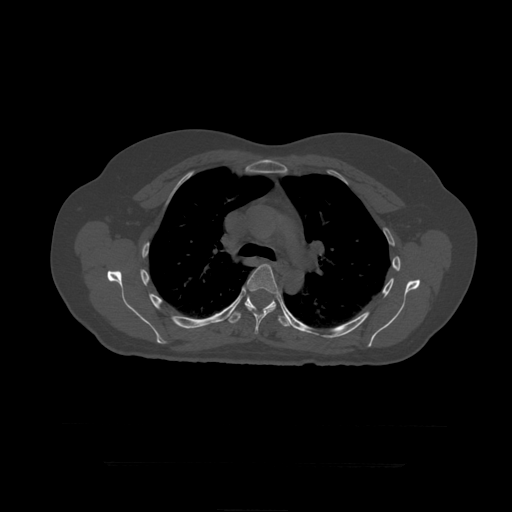
CT including the spine, one axial slice. Slice 313 of 399 in the series (ordered by position). Reconstruction kernel STANDARD. Bone window (W 1800 / L 400 HU). 1.25 mm slice thickness. 512 × 512 image matrix. Patient age 41 years. Case-level facts recorded for this patient, not image findings: primary cancer: breast.
Outlined on this slice (semi-automatically segmented with operator editing):
- T6 vertebra: box from (x=243, y=264) to (x=279, y=335) px
- T7 vertebra: (x=228, y=295)–(x=291, y=327)